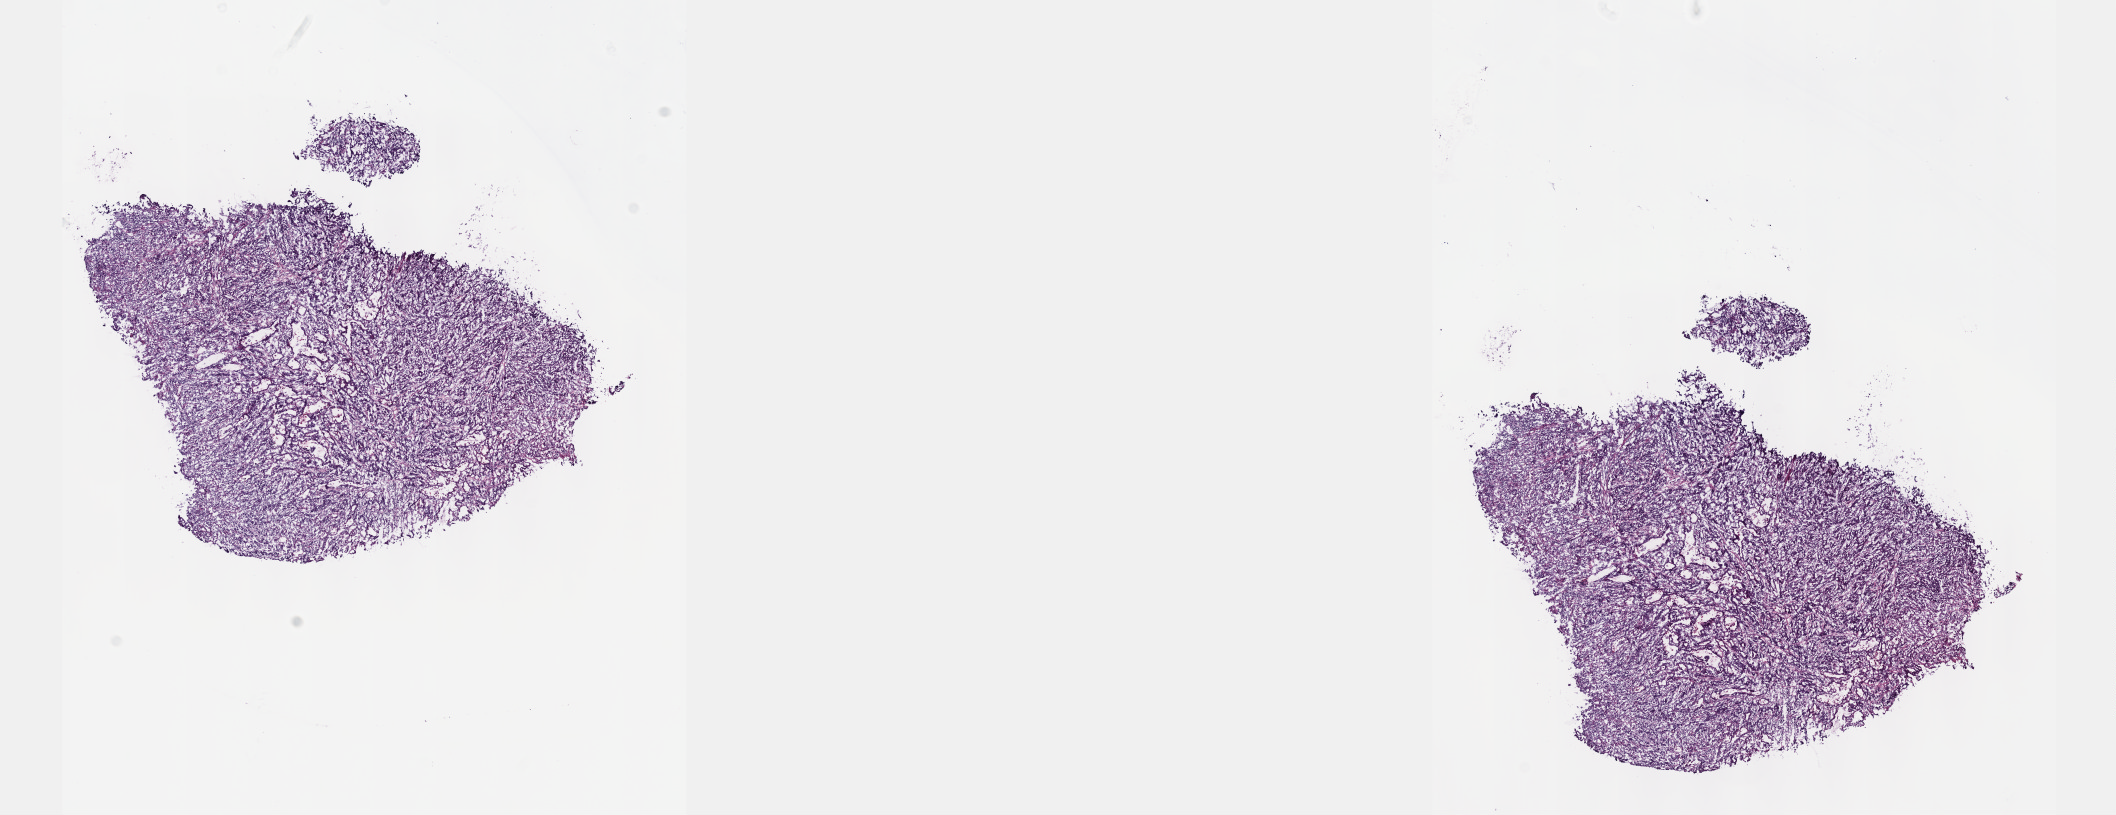
Whole-slide histology image, Hematoxylin and eosin (H&E) stained, shown as a low-resolution overview of the whole scanned area (about 17.1 x 6.6 mm), frozen section from the top of the tissue portion, stomach, primary tumour sample. Patient: male, age at initial diagnosis 74 years. Histologic grade: G3 (poorly differentiated). Slide review estimates, as recorded: tumour cells 75%, tumour nuclei 75%, normal cells 0%, stromal cells 25%, necrosis 0%. Infiltration values recorded for this section: lymphocyte infiltration 3%, monocyte infiltration 2%, neutrophil infiltration 2%.
AJCC pathologic stage: IIB (7th edition). Lymph nodes positive (case pathology): 0 of 26 examined. Diagnosis: Signet ring cell carcinoma (gastric antrum).